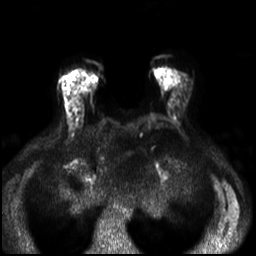
Breast MRI, one axial slice. Slice 13 of 30 in the series (ordered by position). Diffusion-weighted series; image 2 of 4 stored at this slice position (different b-values; order by instance number). 3 T. 4 mm slice thickness. 256 × 256 image matrix. Female patient.
Outlined on this slice (expert manual segmentation):
- tumour on diffusion-weighted imaging: bounding box (x1, y1, x2, y2) in pixels: (69, 93, 81, 110)